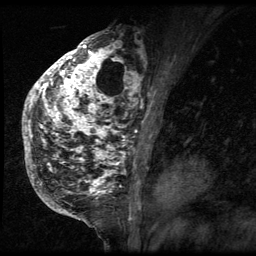
Breast MRI (dynamic contrast-enhanced), one sagittal slice; slice 36 of 64 in the series (ordered by position); 3 images stored at this slice position (order not interpretable as contrast timing); 1.5 T; TE 4.2 ms, TR 9 ms; 256 × 256 image matrix, field of view 180 × 180 mm. Patient: female, 50 years. From the clinical record (not read from this slice): setting: breast cancer imaged before/during neoadjuvant chemotherapy; receptor status: triple-negative.
Outlined on this slice (semi-automatic segmentation, software-assisted and operator-edited):
- analysis volume of interest (the breast-tissue region the enhancement analysis was run in; not a lesion): bounding box <24,39,140,212> (left, top, right, bottom; pixels)
- tumour enhancement mask (voxels above the 140 % enhancement threshold inside the analysis volume of interest): <24,39,140,208>